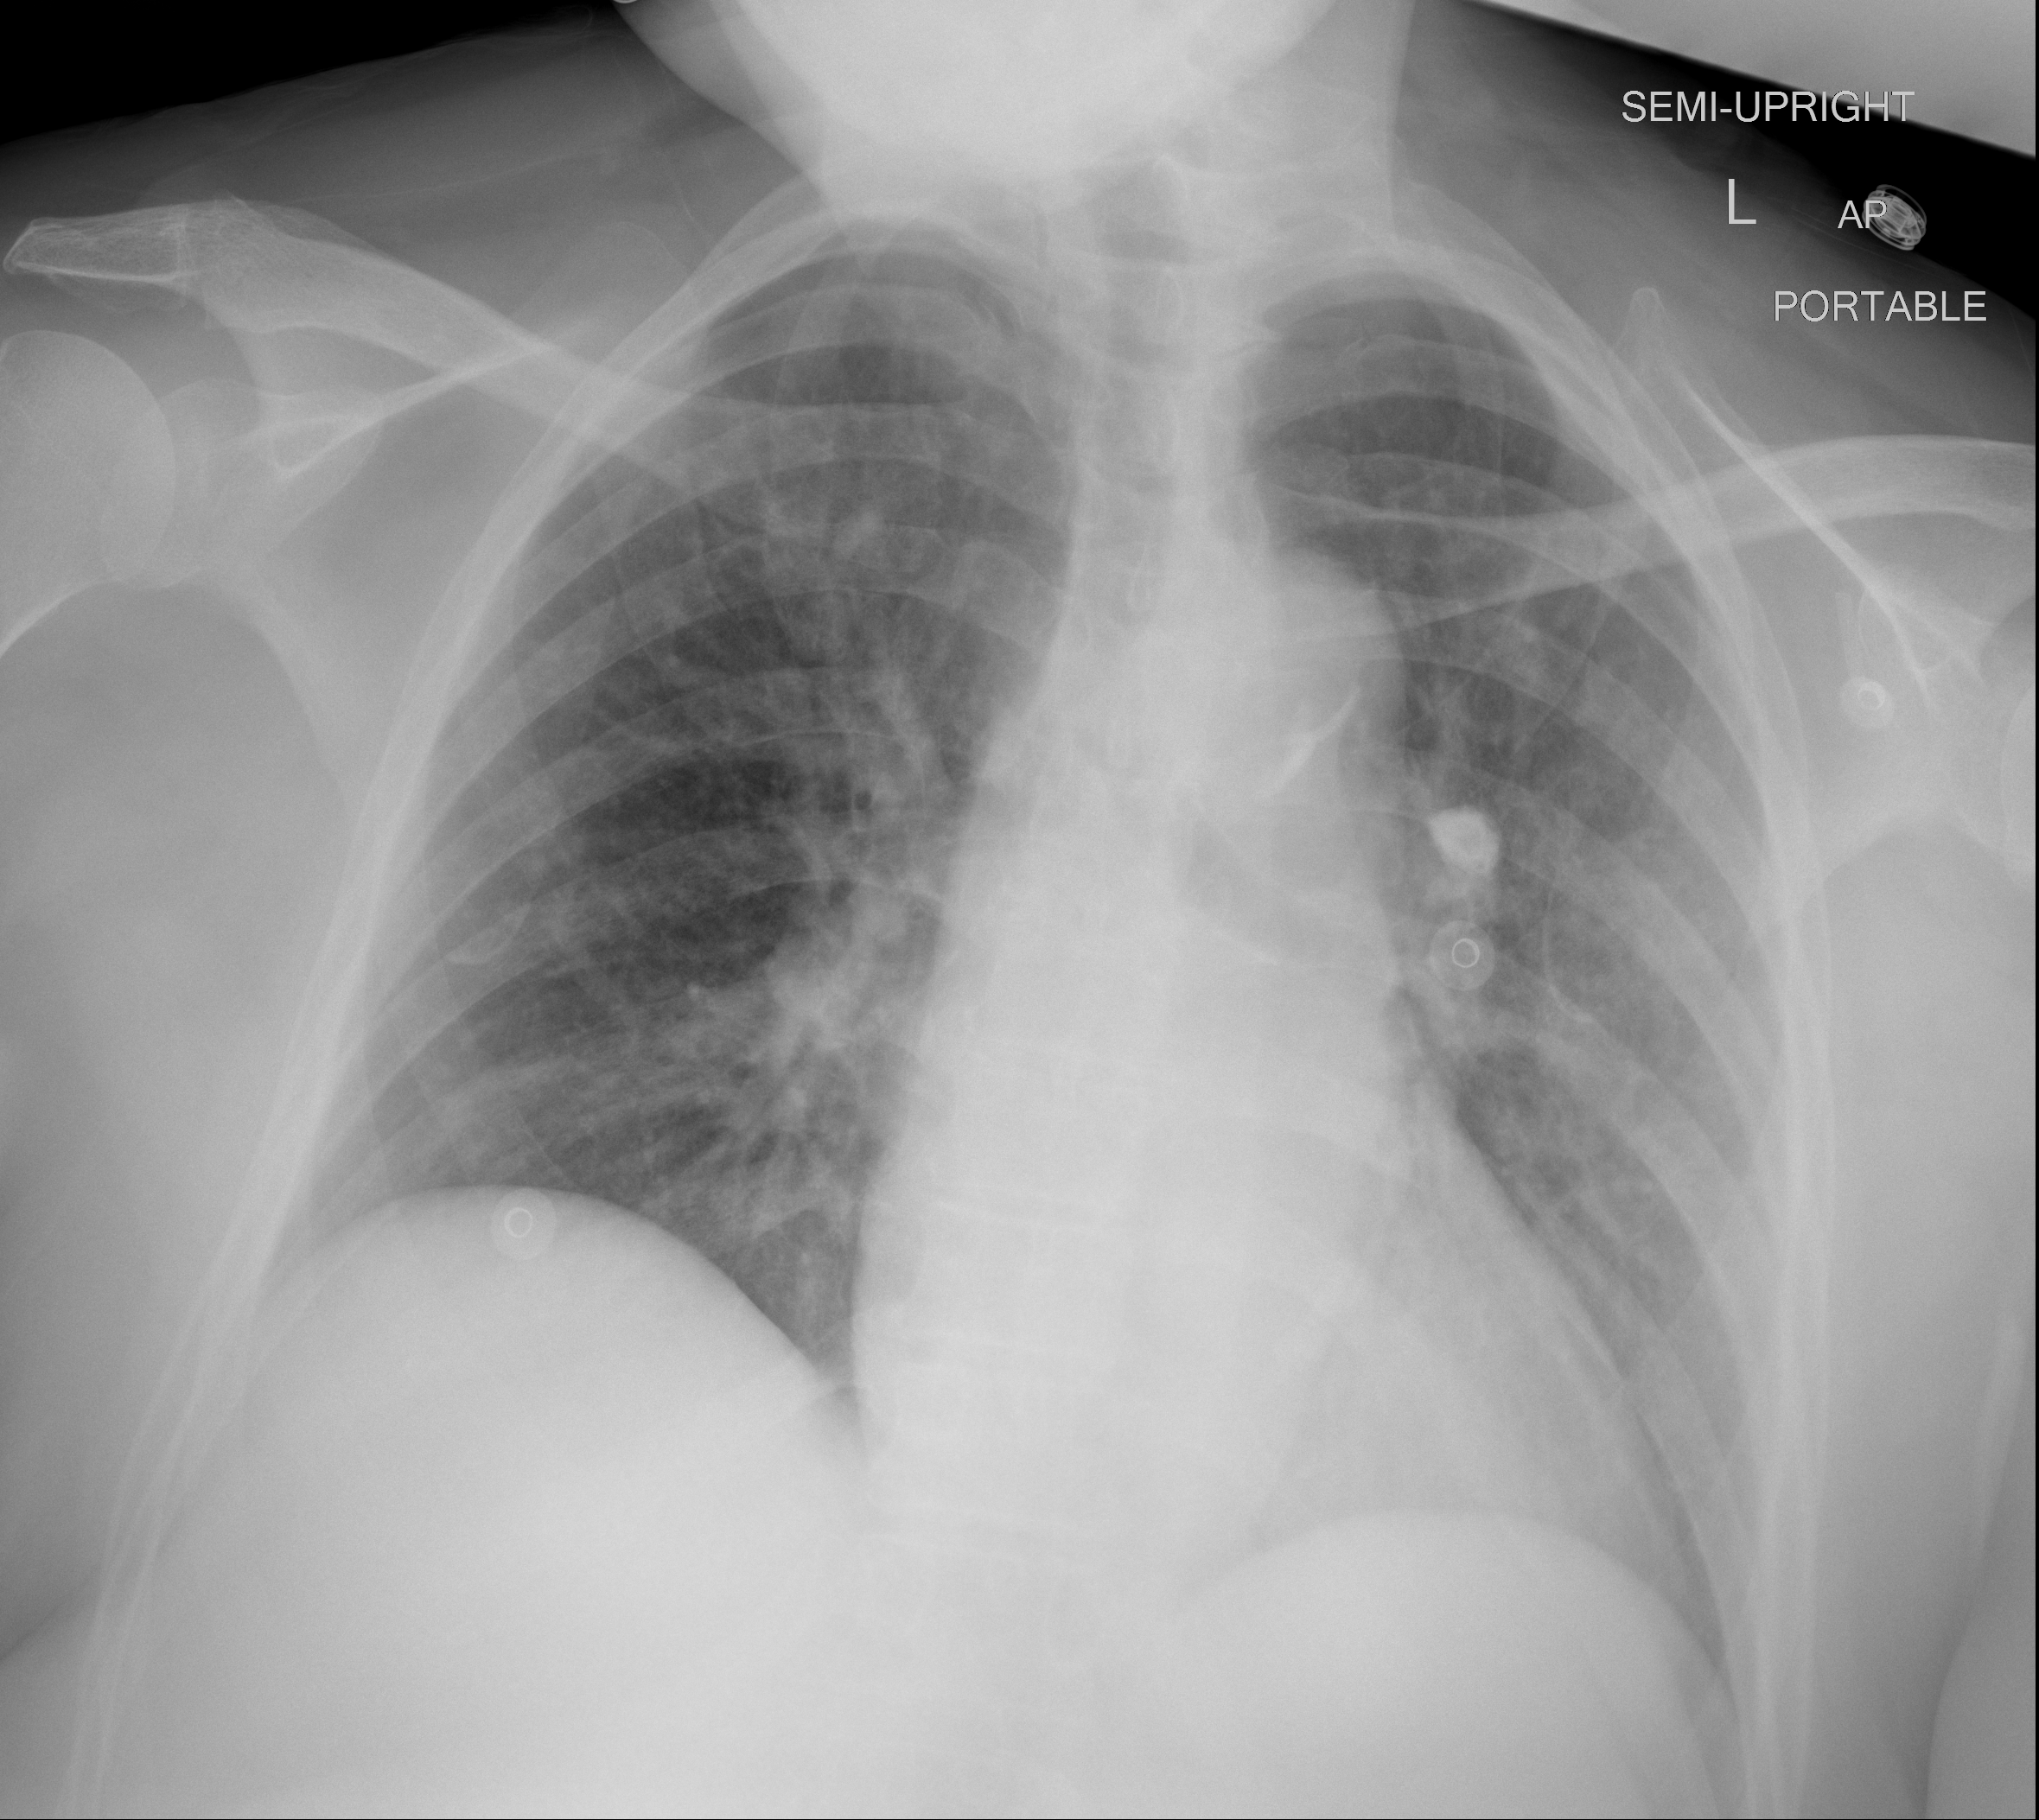
Portable chest radiograph, AP projection. Female patient, age 64 years; imaged 1 day after the COVID-19 diagnosis.
Radiologist key findings (as recorded): No definite acute cardiopulmonary findings.